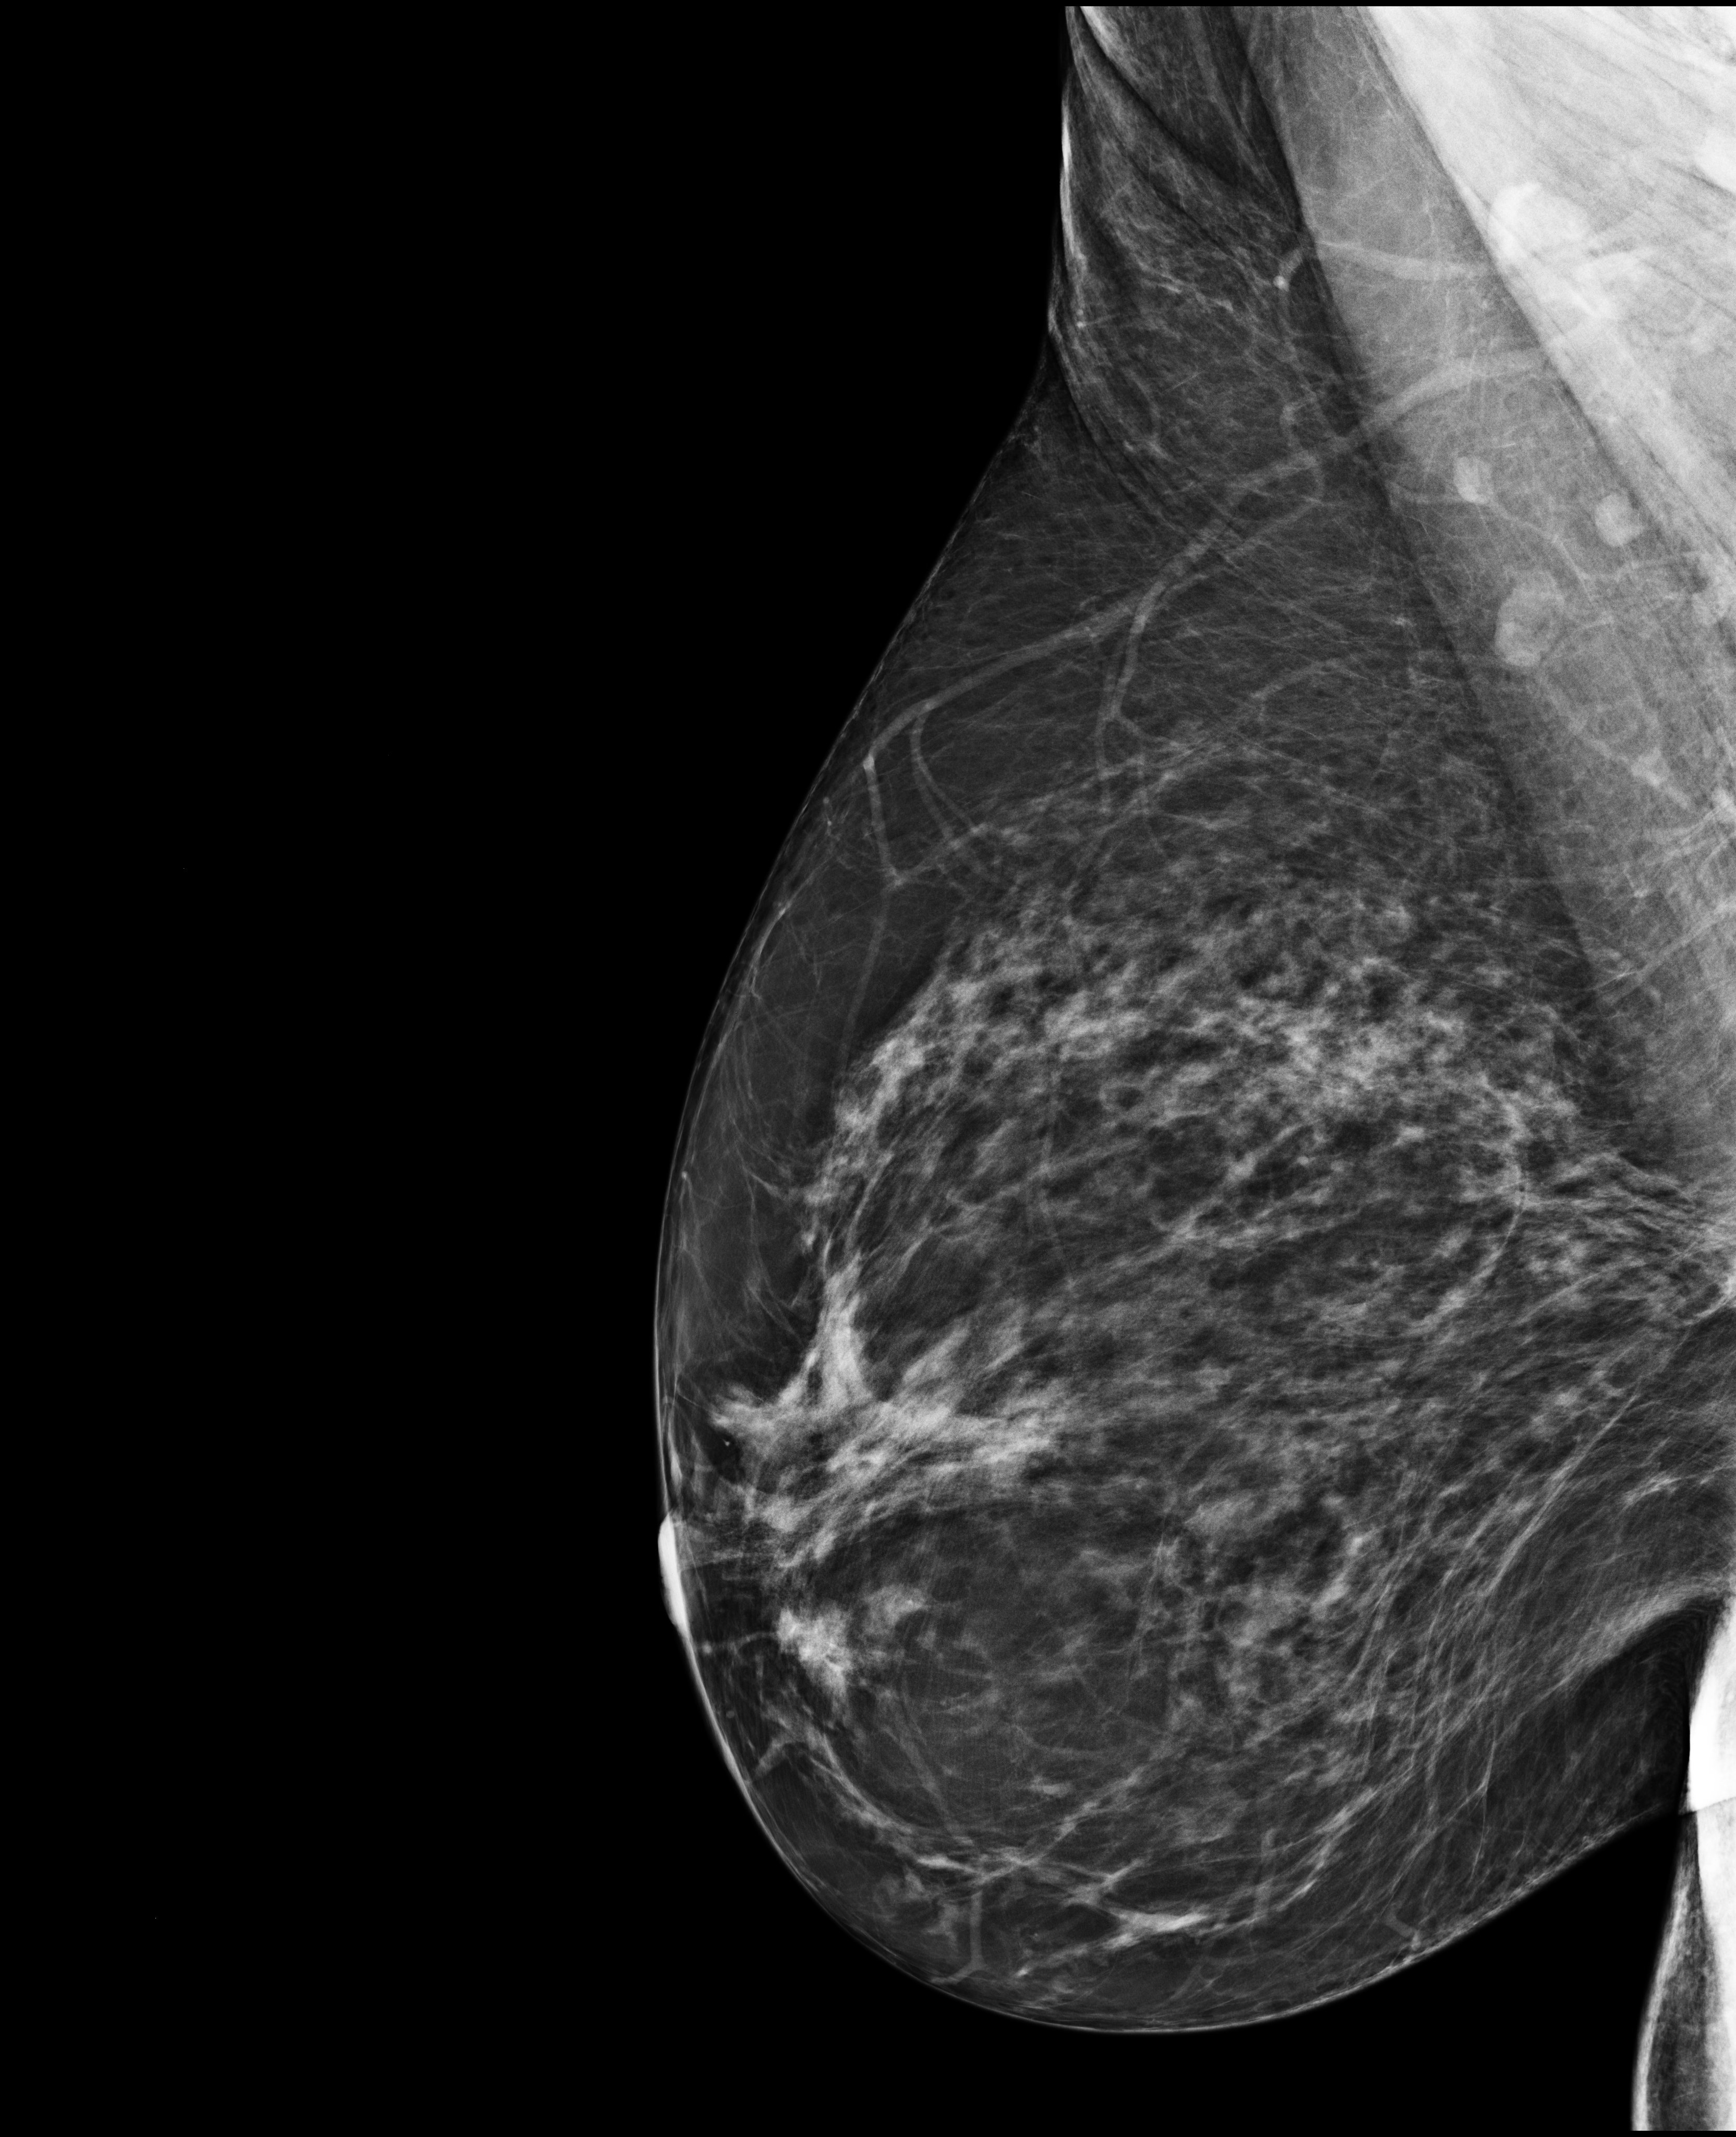
Annual screening mammography examination, compressed breast thickness 82 mm, system: Selenia Dimensions.
Image type: full-field digital mammogram. Breast: right. Projection: mediolateral oblique (MLO) view.